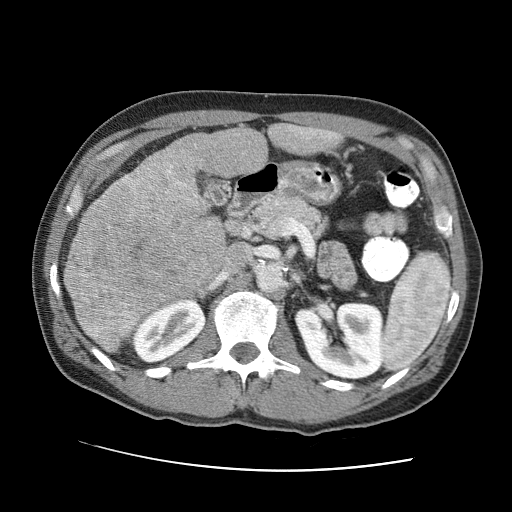
Contrast-enhanced abdominal CT (liver protocol), one axial slice; position 37 of 95 along the scan axis; reconstruction kernel STANDARD; 120 kVp; one of 2 acquisitions stored at this slice position; soft-tissue window (W 400 / L 40 HU); 2.5 mm slice thickness; 512 × 512 image matrix, field of view 360 × 360 mm. Case-level facts recorded for this patient, not image findings: diagnosis: hepatocellular carcinoma (patient treated with transarterial chemoembolisation; whether this scan precedes or follows treatment is not stated here); TNM stage (as recorded): Stage-IVA; Child-Pugh class: A; tumour differentiation: moderately differentiated; tumour nodularity: multinodular.
Structures marked on this image (semi-automatic segmentation, software-assisted and operator-edited):
- liver parenchyma outside the tumour (the mass and vessels are separate outlines, so this box may not span the whole liver): bounding box <64,124,342,328> (left, top, right, bottom; pixels)
- mass: <64,146,225,353>
- liver vessels: <288,126,337,140>